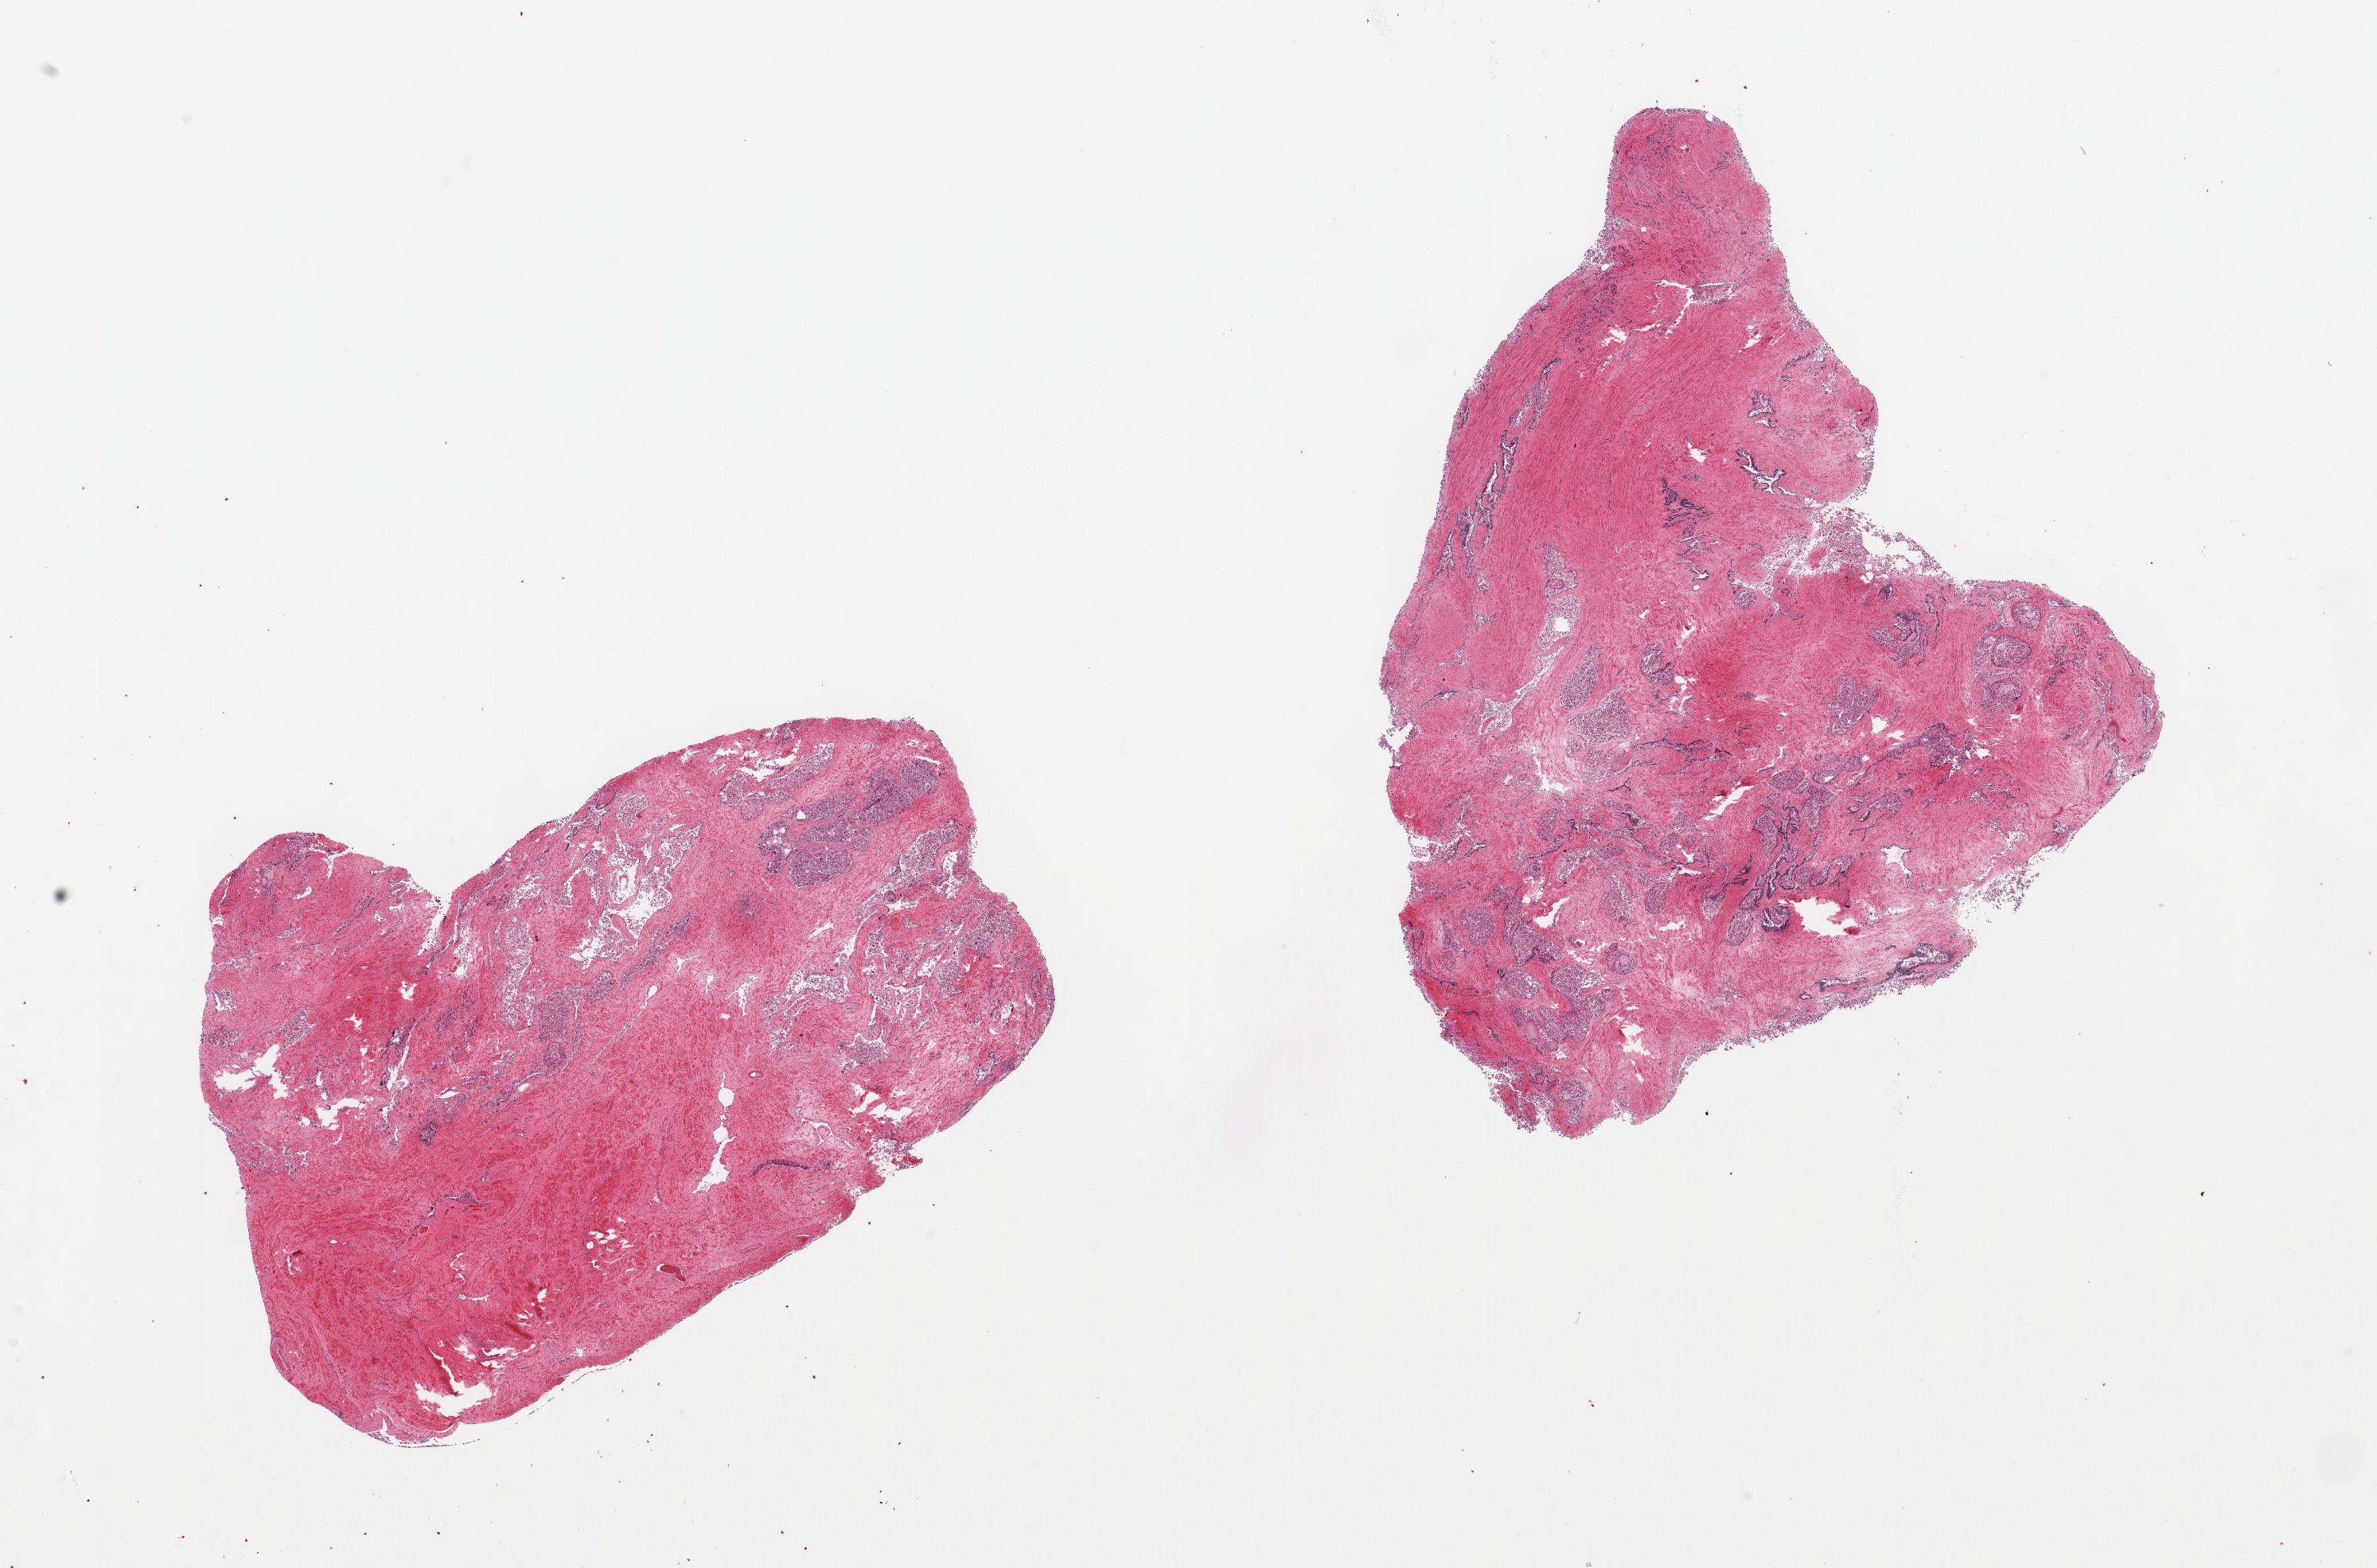
Whole-slide image, H&E stain — low-resolution overview of the scanned area, about 23.6 x 15.6 mm, PAXgene-fixed paraffin-embedded (PFPE) section, section of prostate (target tissue), tissue donor sample. Donor: male.
Reviewer comment on this tissue sample: 2 aliquots. ~9x7mm. Glands severely autolyzed.